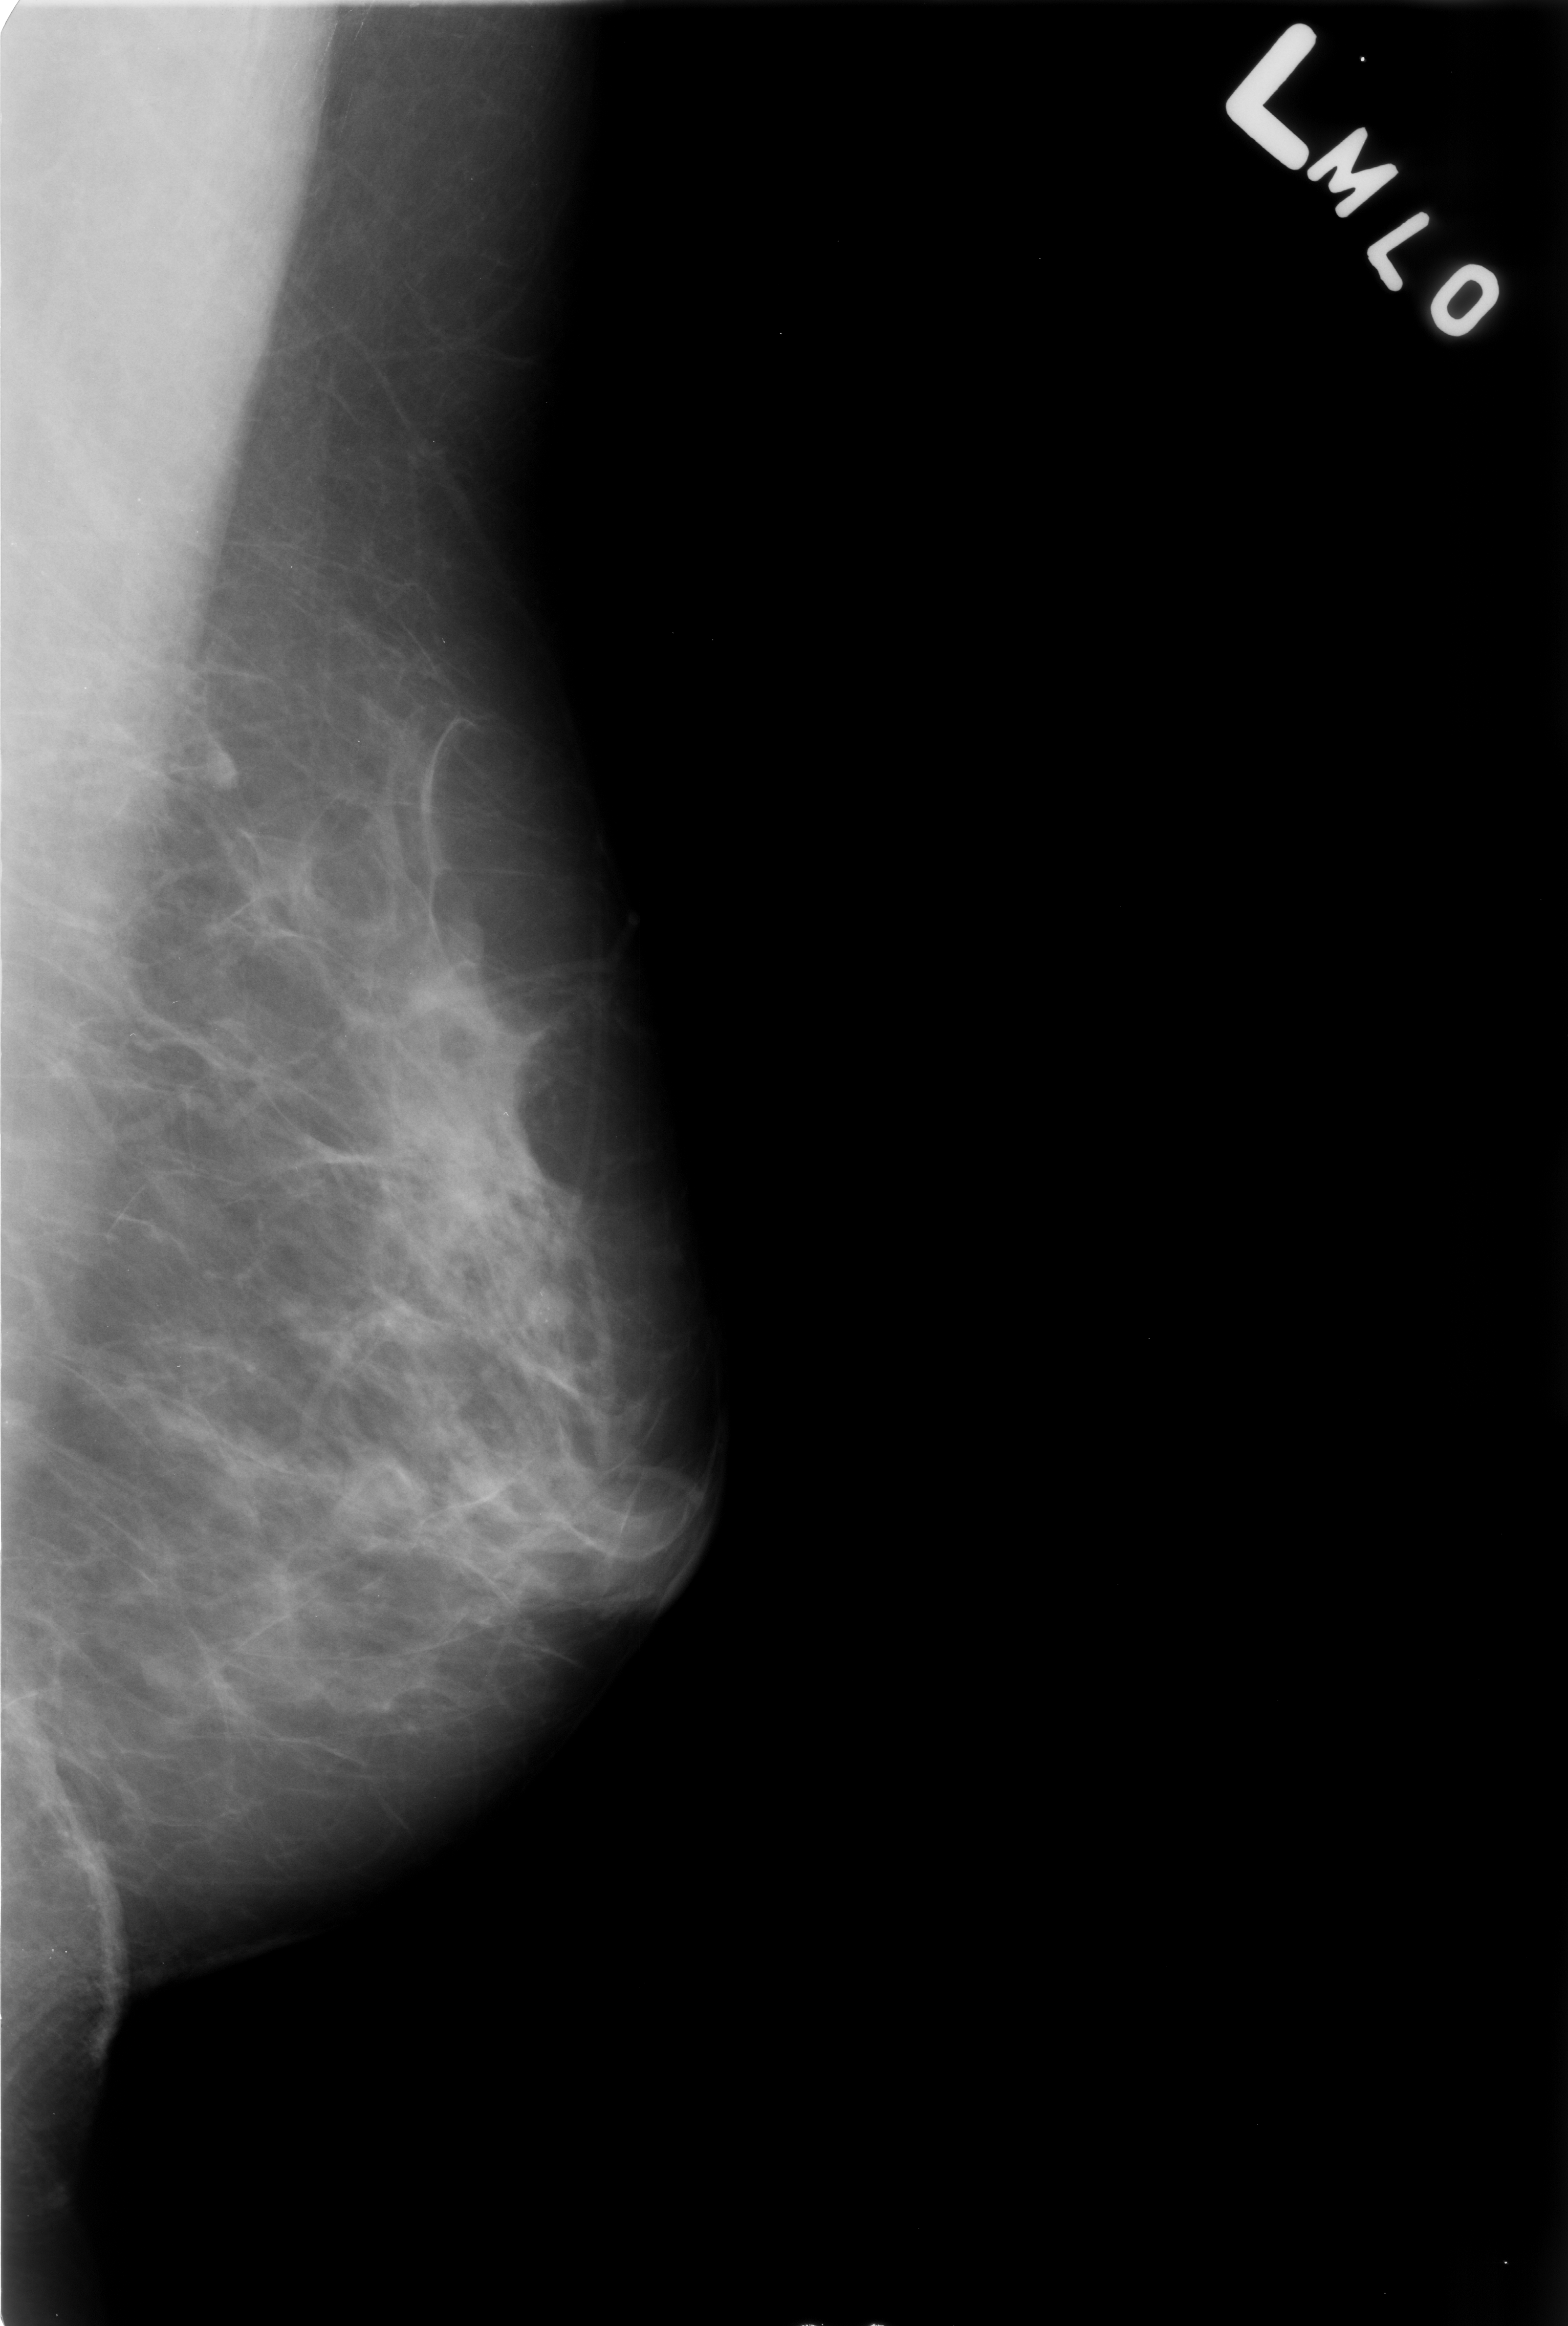
Digitized screen-film mammogram; left breast; mediolateral oblique (MLO) view; breast composition: scattered fibroglandular densities (BI-RADS density category 2 of 4).
Abnormality record for this image: calcifications, morphology punctate / pleomorphic, distribution clustered; BI-RADS assessment category 4; subtlety rating 3 on a 1 (subtle) to 5 (obvious) scale; pathology (as recorded): benign.